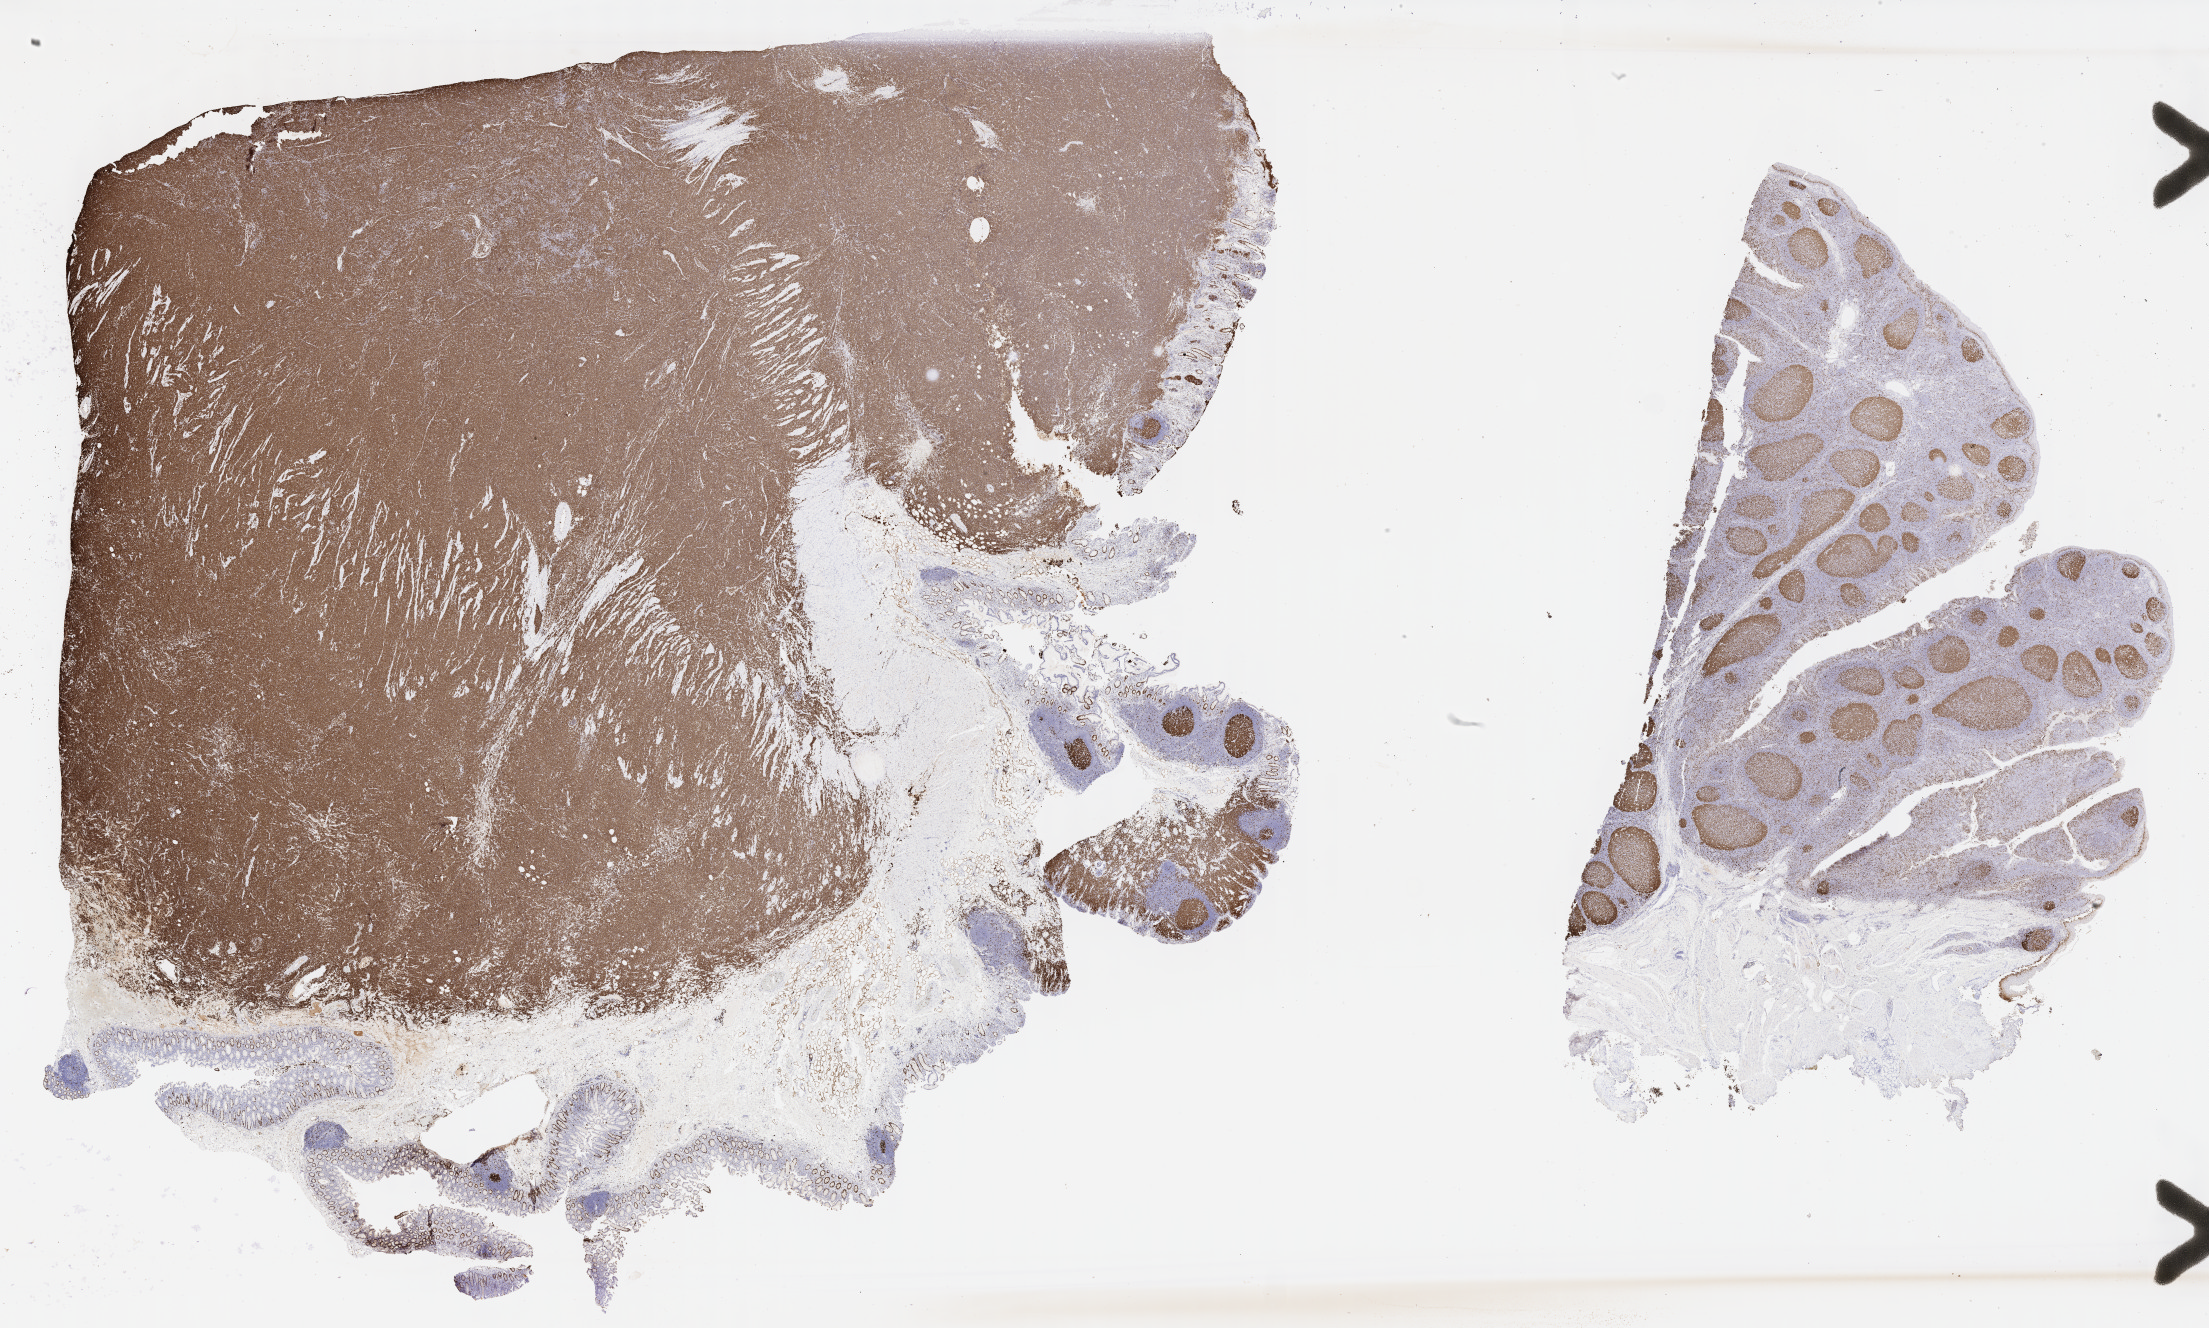
Immunohistochemistry (IHC) whole-slide image stained for Ki-67, shown as a low-resolution overview of the whole scanned area (about 35.7 x 21.5 mm), specimen: tumor tissue. Patient male; 59 years old.
* histologic diagnosis: Burkitt lymphoma, NOS